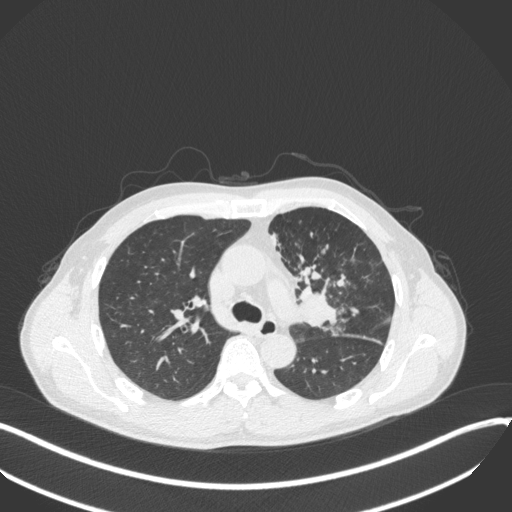
Chest CT, one axial slice. Position 226 of 411 along the scan axis. 120 kVp. Lung window (W 1500 / L -600 HU). 1 mm slice thickness. 512 × 512 image matrix, field of view 400 × 400 mm. Patient: male, 56 years. Case-level facts recorded for this patient, not image findings: clinical TNM (as recorded): T2a N0 M0.
Annotated regions visible in this slice (rectangle marked by the reading radiologist):
- lung tumour (recorded histology: squamous cell carcinoma): bounding box (x1, y1, x2, y2) in pixels: (298, 278, 346, 333)